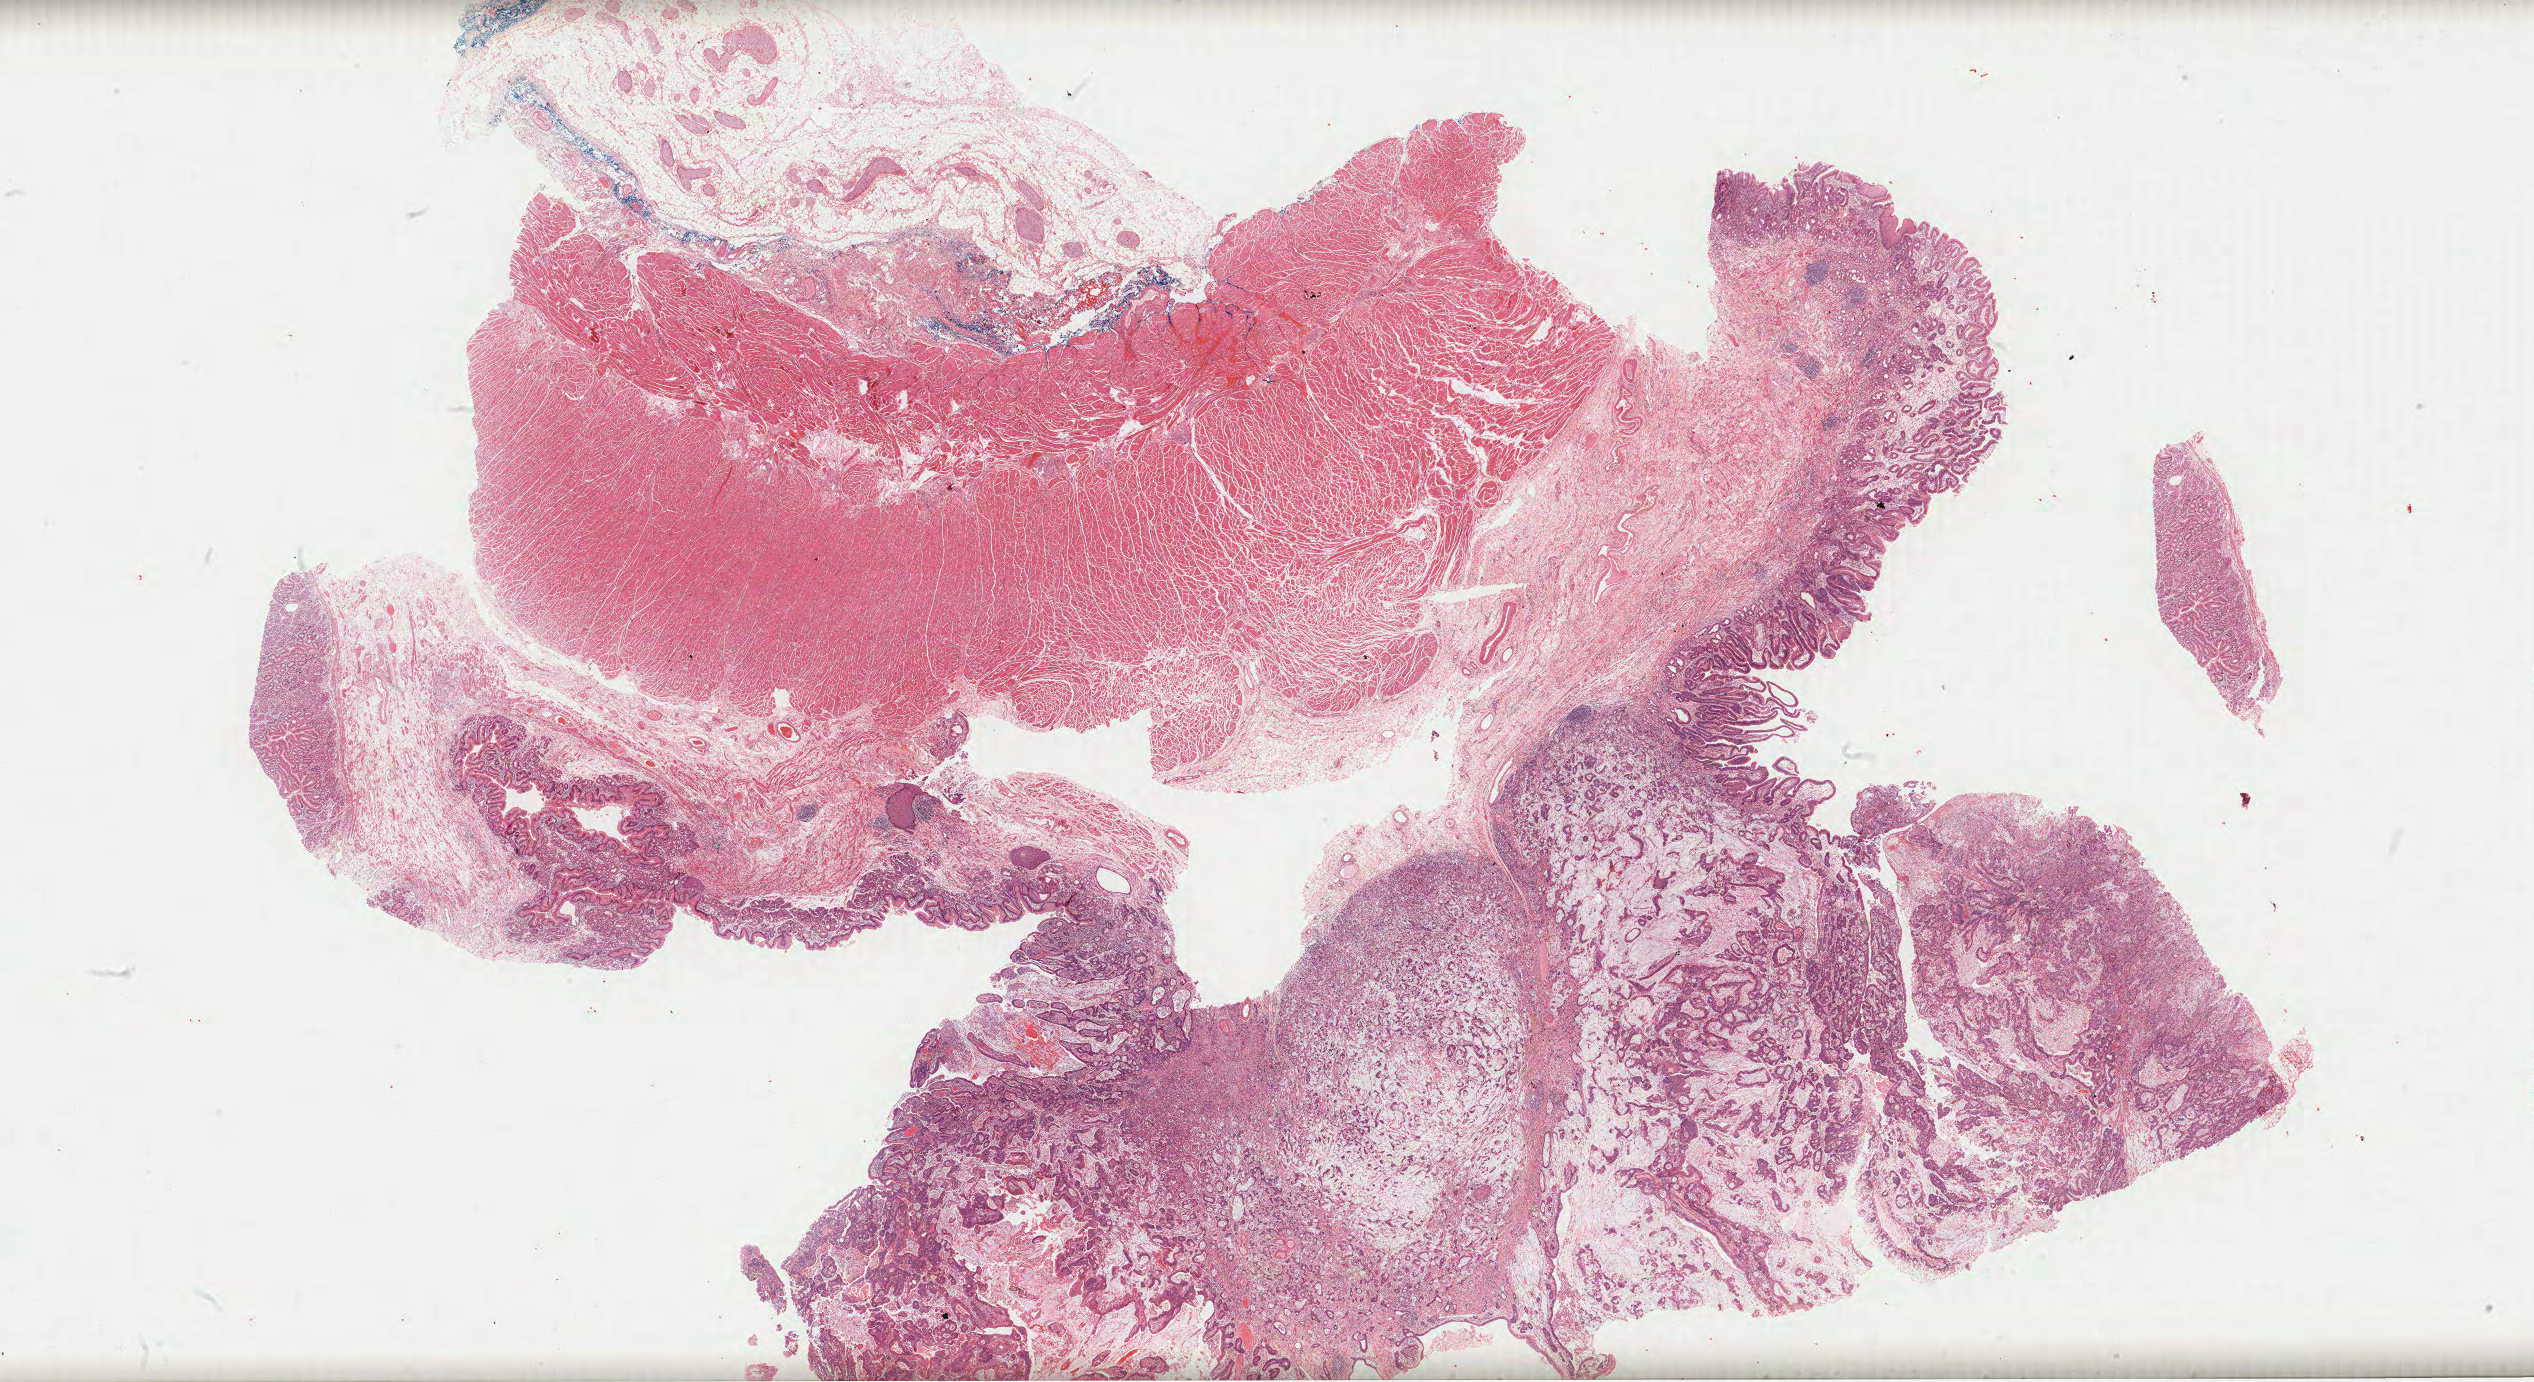
Whole-slide histology image, Hematoxylin and eosin (H&E) stained — shown as a low-resolution overview of the whole scanned area (about 40.7 x 22.2 mm). Formalin-fixed paraffin-embedded (FFPE) diagnostic section. Esophagus, primary tumour sample. Patient: female, age at initial diagnosis 72 years. Histologic grade: G3 (poorly differentiated).
• AJCC pathologic stage: IIB
• histologic diagnosis: Adenocarcinoma, NOS (lower third of esophagus)